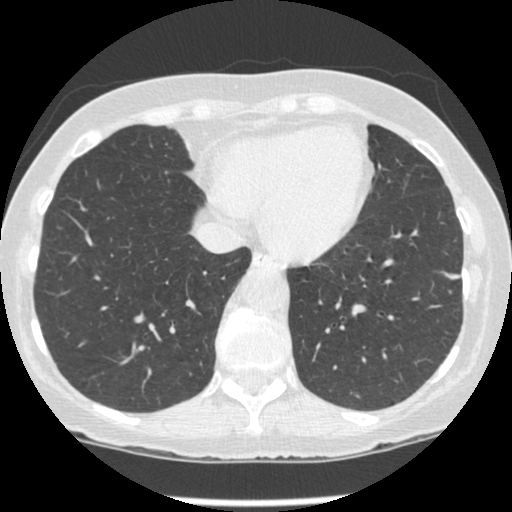
Low-dose screening chest CT, one axial slice. Position 72 of 247 along the scan axis. Reconstruction kernel STANDARD. Lung window (W 1500 / L -600 HU). 1.25 mm slice thickness. 512 × 512 image matrix, field of view 303 × 303 mm.
Structures marked on this image (manually delineated by an expert):
- lesion 1 (tumor, lower lobe of left lung): bounding box [x1, y1, x2, y2] px = [445, 273, 460, 280]